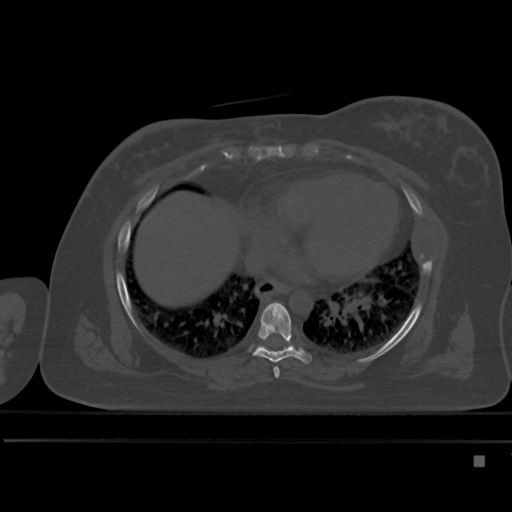
CT including the spine, one axial slice. Slice 291 of 495 in the series (ordered by position). Bone window (W 1800 / L 400 HU). 1.5 mm slice thickness. 512 × 512 image matrix, field of view 404 × 404 mm. Patient: female, 33 years. From the clinical record (not read from this slice): primary cancer: breast.
Outlined on this slice (semi-automatically segmented with operator editing):
- T6 vertebra: box from (x=273, y=367) to (x=280, y=378) px
- T7 vertebra: (x=253, y=302)–(x=311, y=364)
- T8 vertebra: (x=258, y=346)–(x=267, y=350)